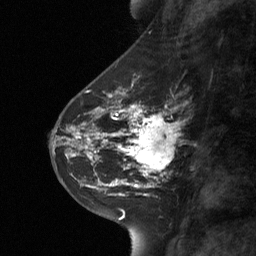
Breast MRI (dynamic contrast-enhanced), one sagittal slice. Position 27 of 64 along the scan axis. Dynamic contrast-enhanced study with each time point stored as its own series, time point 2 of 3 at this slice position (early post-contrast, ordered by acquisition time). 1.5 T. TE 4.8 ms, TR 27 ms. 2 mm slice thickness. 256 × 256 image matrix, field of view 180 × 180 mm. Patient: female, 42 years. From the clinical record (not read from this slice): setting: breast cancer imaged before/during neoadjuvant chemotherapy; receptor status: triple-negative.
Outlined on this slice (semi-automatically segmented with operator editing):
- analysis volume of interest (the breast-tissue region the enhancement analysis was run in; not a lesion): bounding box (x1, y1, x2, y2) in pixels: (111, 104, 176, 178)
- tumour enhancement mask (voxels above the 90 % enhancement threshold inside the analysis volume of interest): (118, 105, 175, 175)